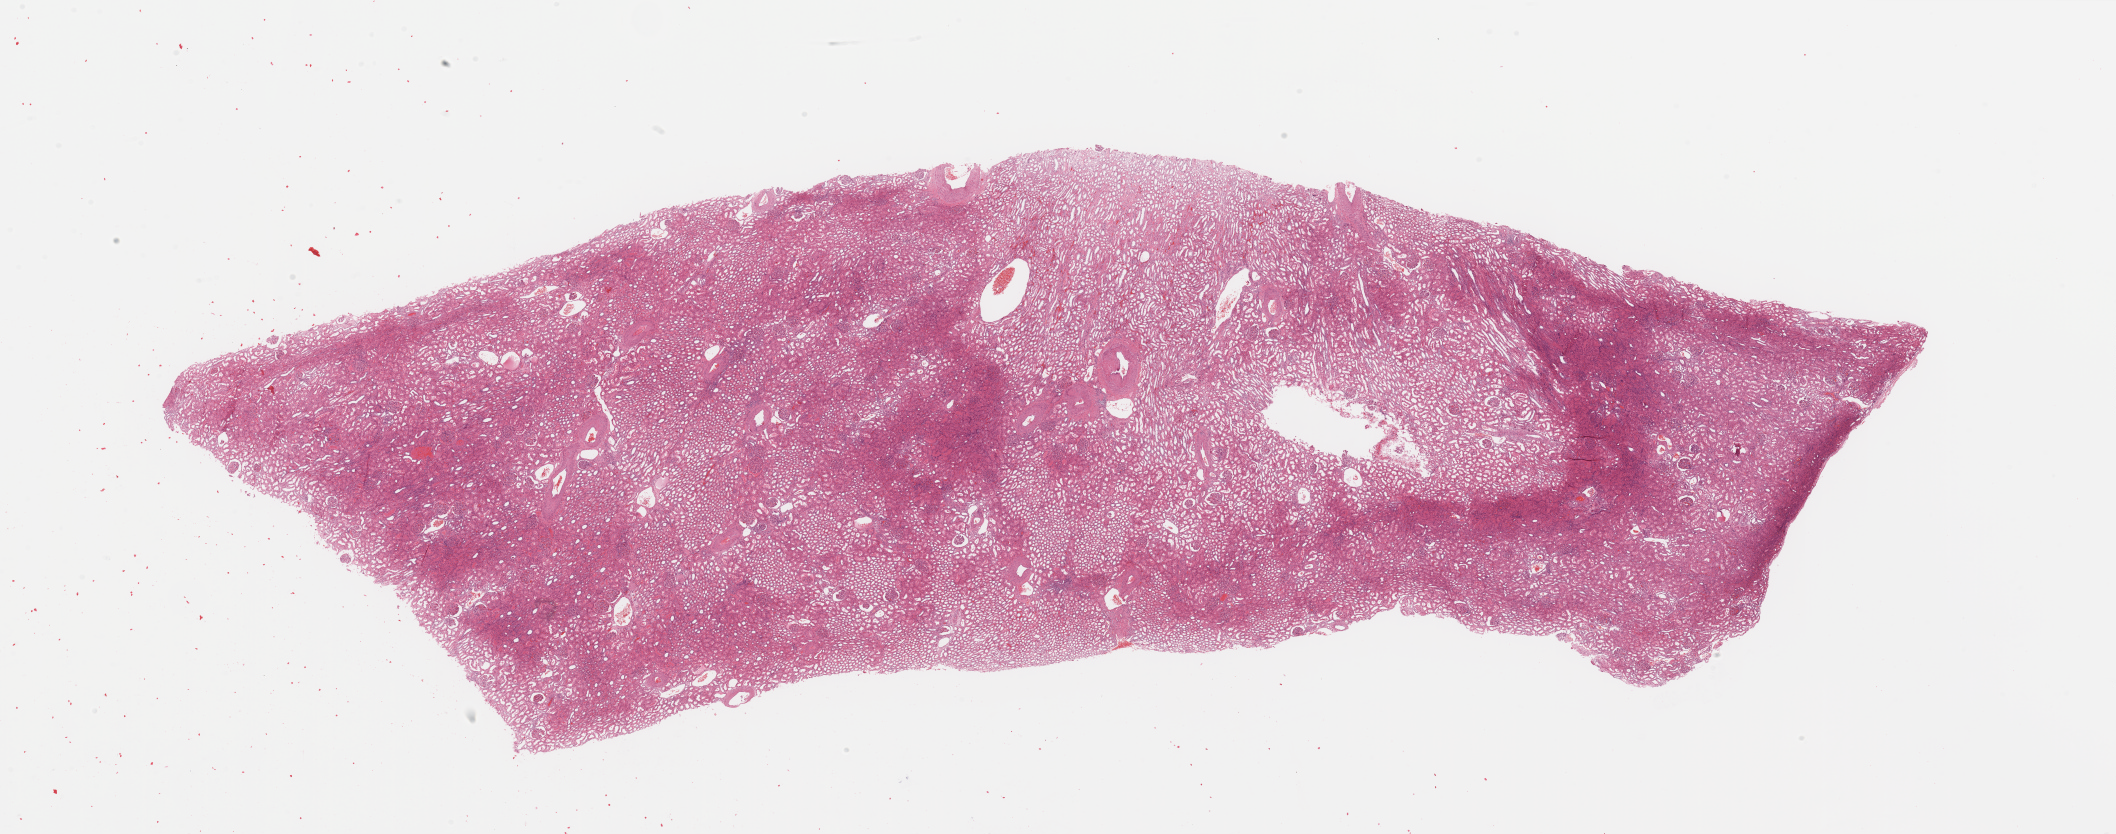
H&E-stained whole-slide image — whole scanned area (about 33.5 x 13.2 mm) shown as a low-resolution overview, normal (non-tumour) tissue sample, sampled site: kidney. Male, 61 y/o.
This section: normal (non-tumour) tissue from the same patient. Patient diagnosis: Renal cell carcinoma, NOS.